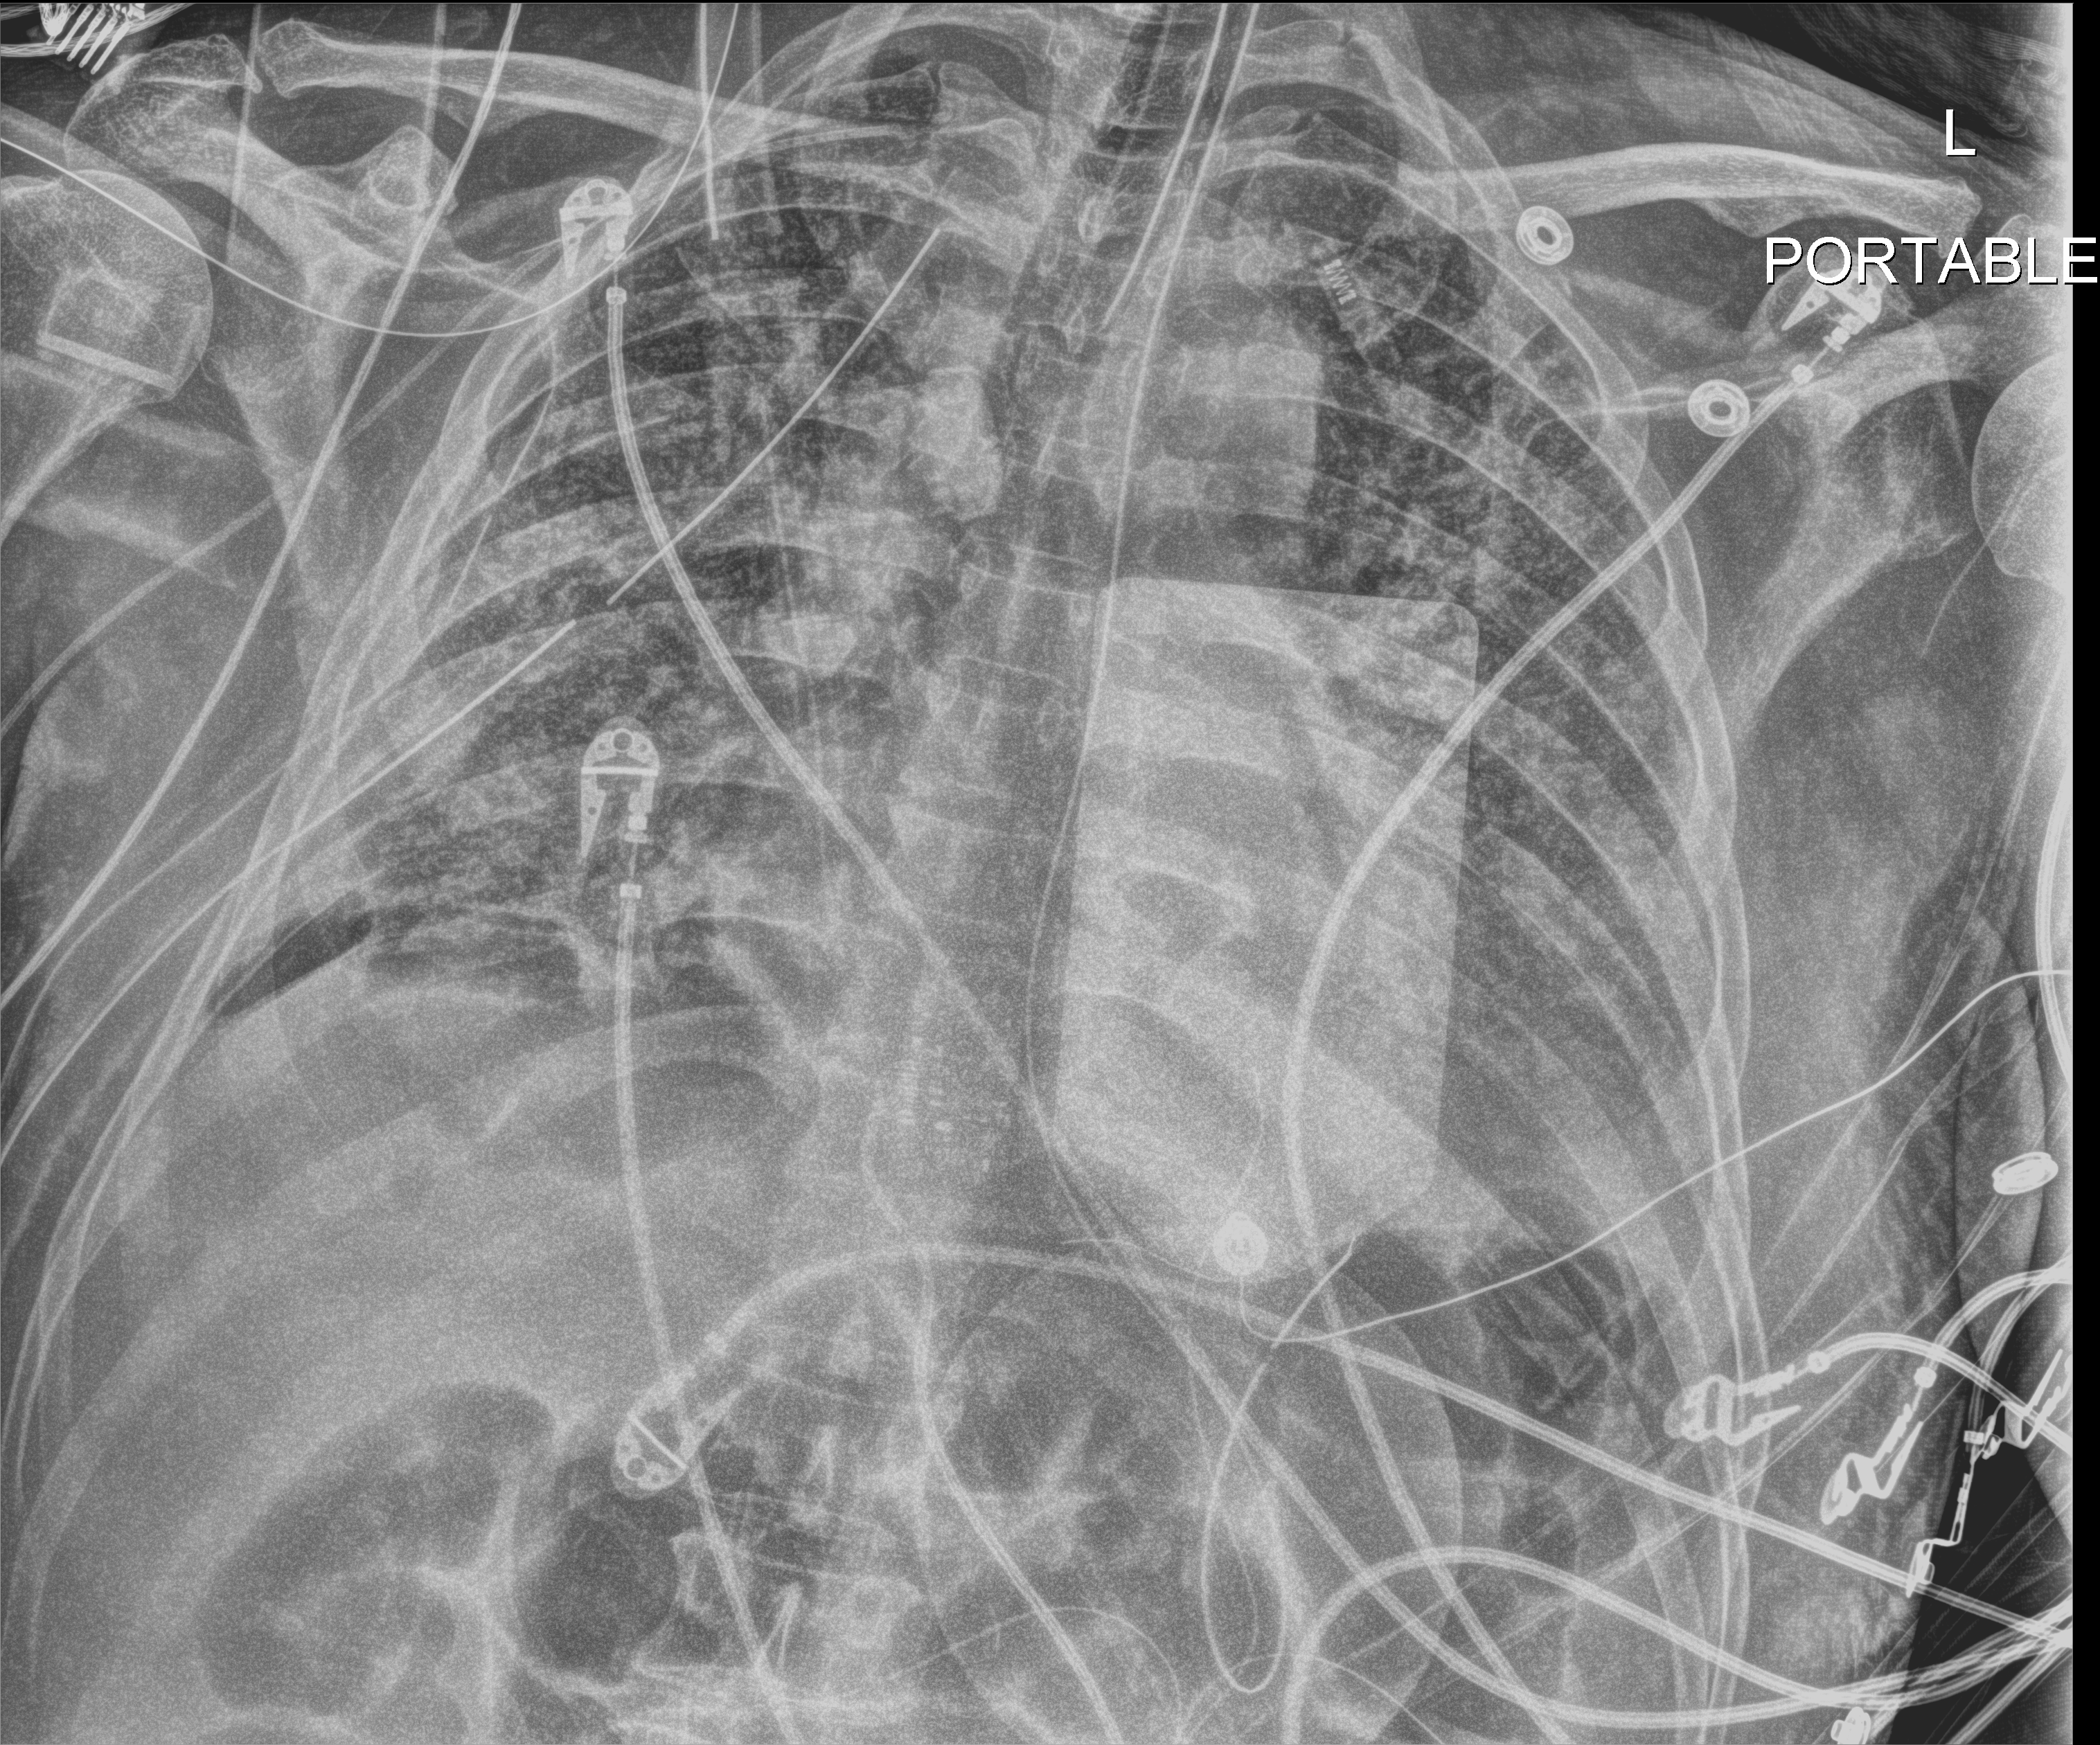
Chest radiograph. Male patient hospitalised with COVID-19, age 60–74 years.
Hospital-stay facts (about this admission, not read from this image; timing relative to this image not recorded): mechanically ventilated during this hospital stay: yes; admitted to intensive care during this hospital stay: yes; diabetes (admission record): yes.